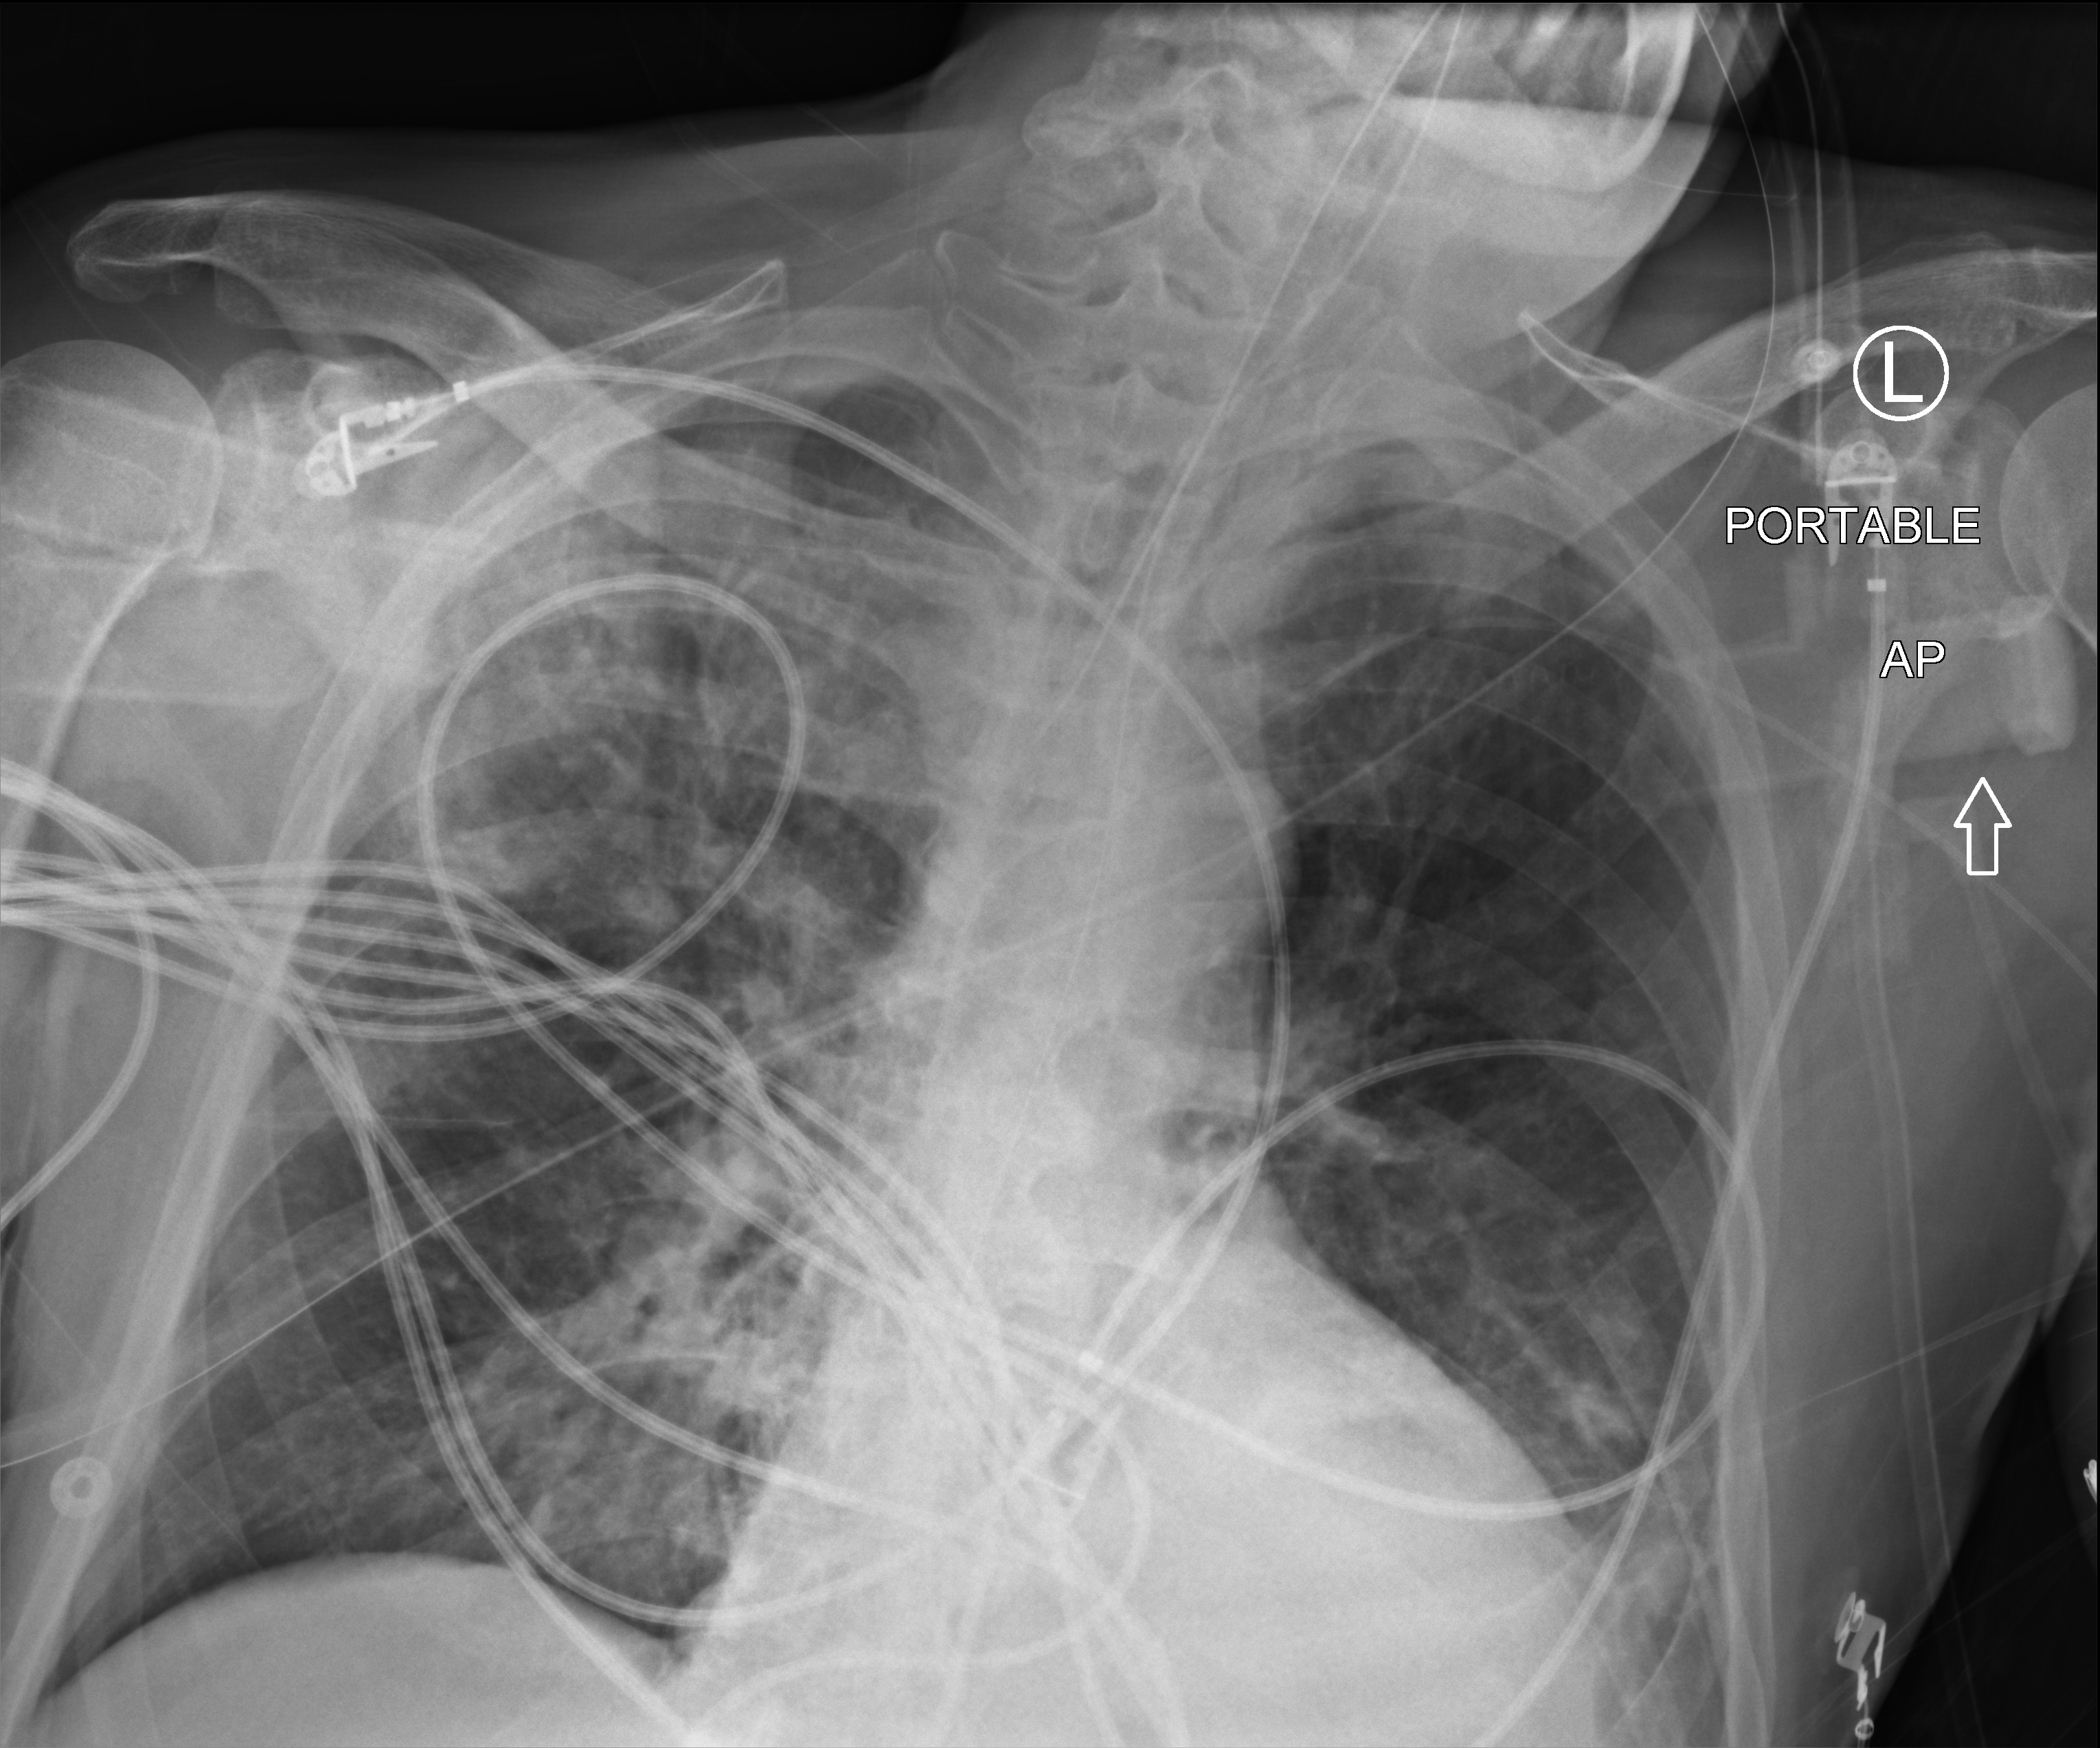
Chest X-ray (portable), anteroposterior (AP) projection. Male patient hospitalised with COVID-19, age 60–74 years.
Admission-level facts for this patient (not findings on this image; timing relative to this image not recorded): hypertension (admission record): yes; diabetes (admission record): yes.